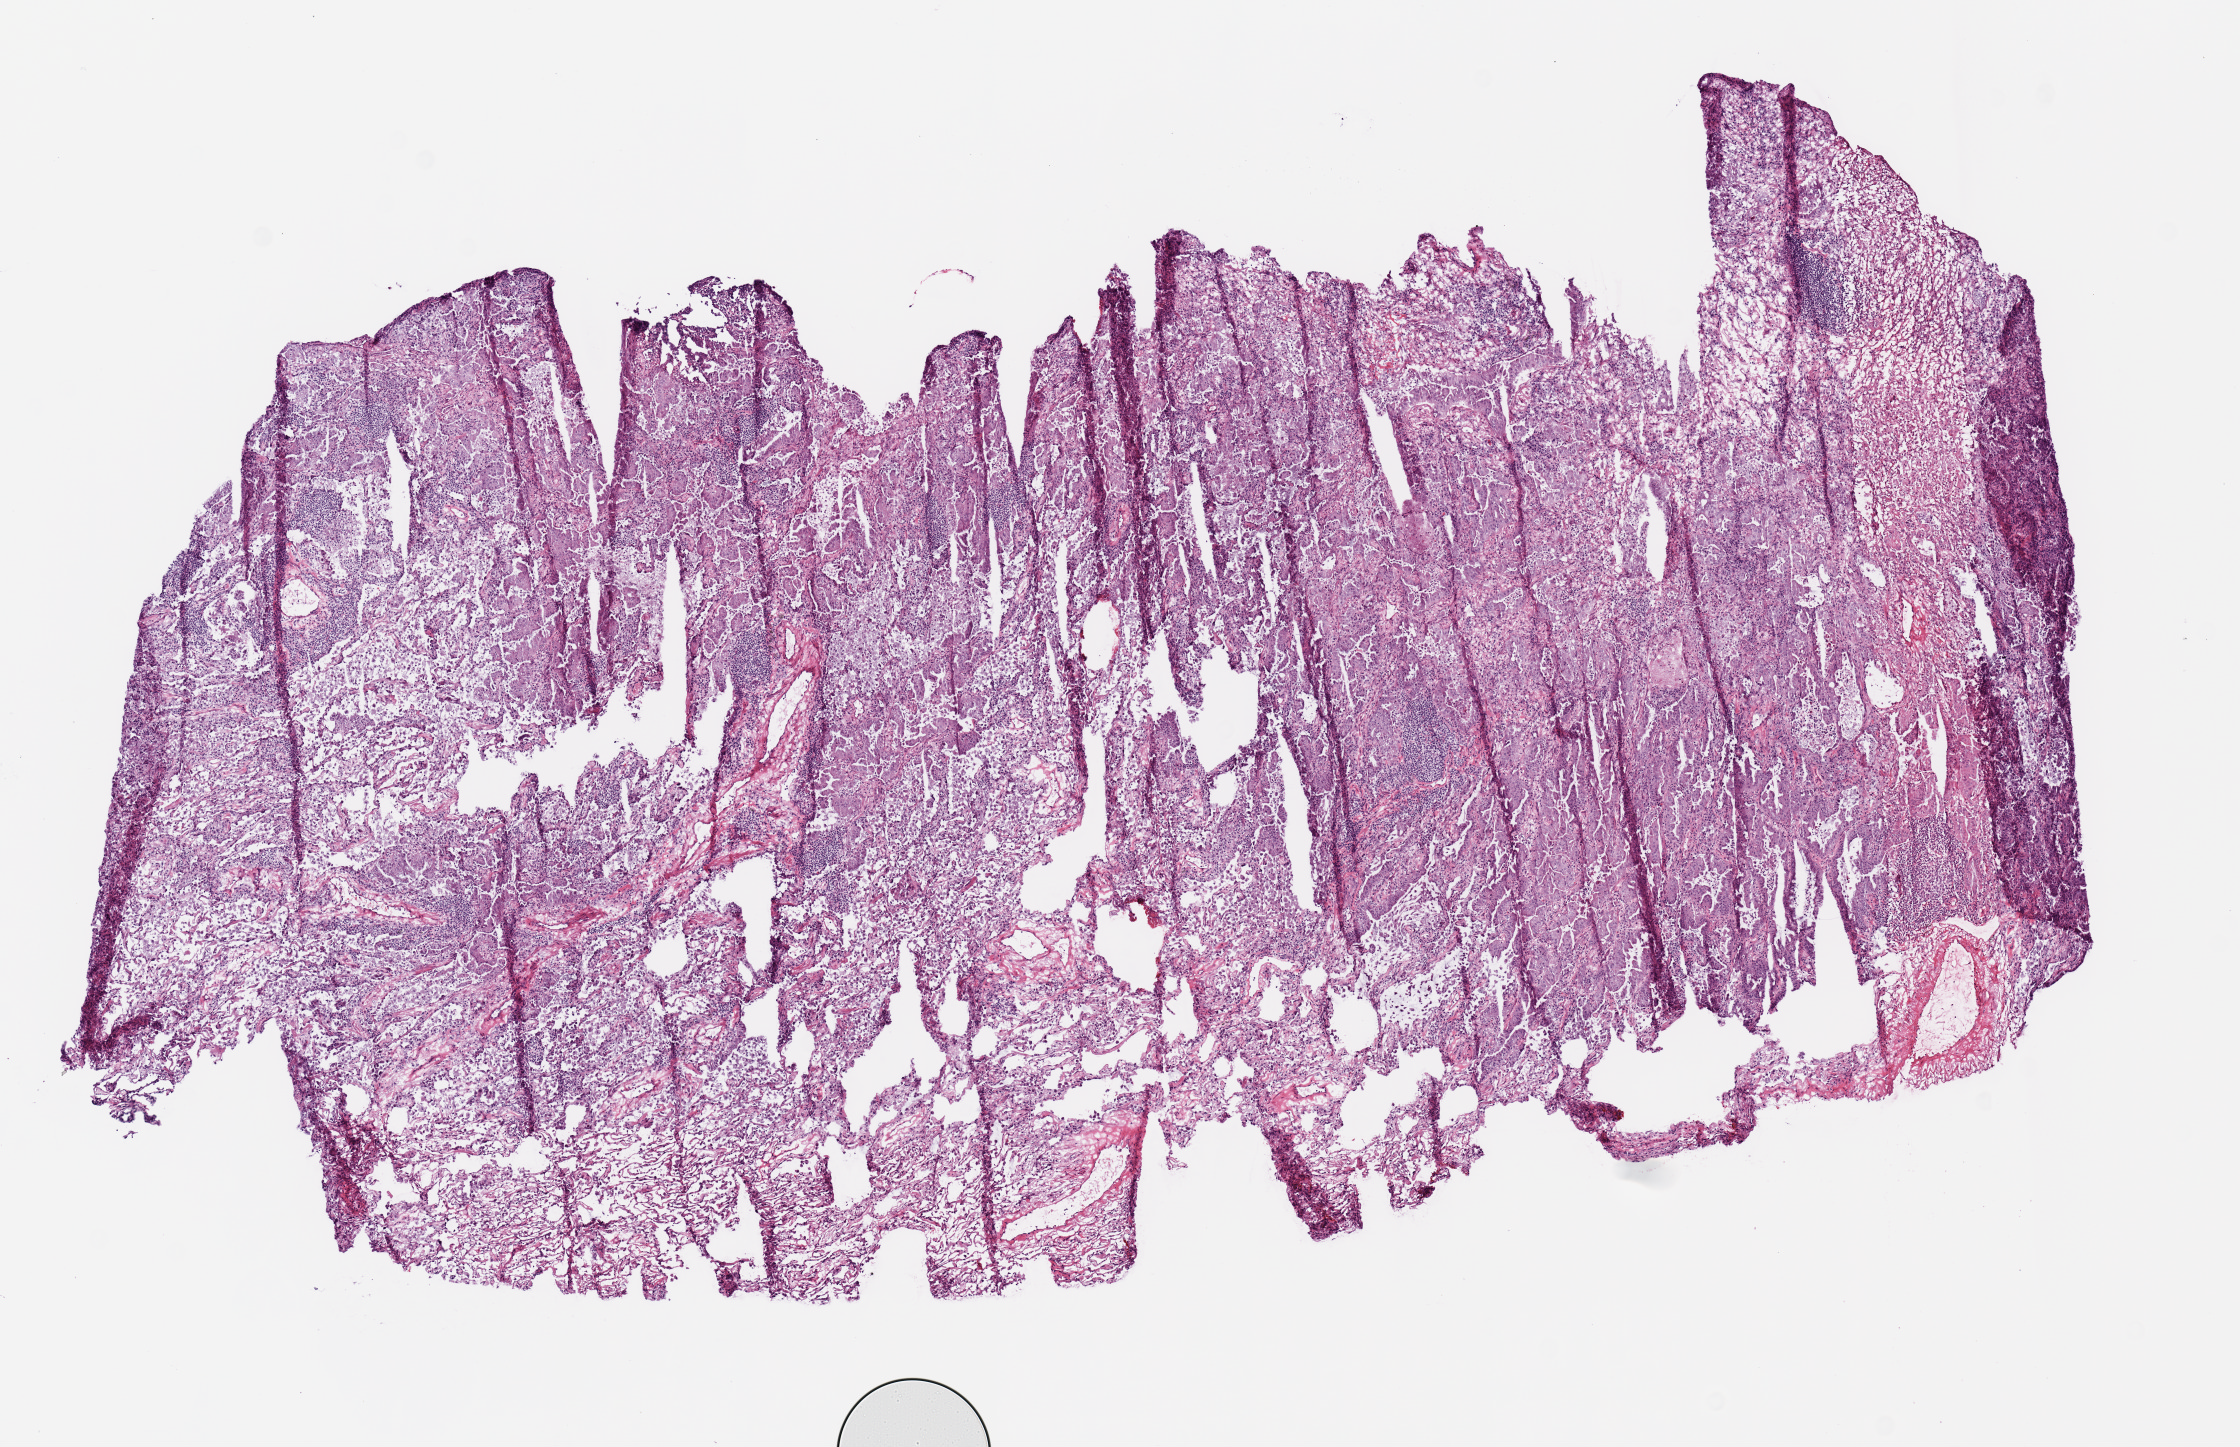
Digitized Hematoxylin and eosin (H&E) stained tissue section (whole slide) — whole scanned area (about 8.9 x 5.7 mm, from a 20x scan) shown as a low-resolution overview; frozen section from the top of the tissue portion; lung, primary tumour sample. Female patient; age at initial diagnosis 72 years. Slide review estimates, as recorded: tumour cells 72%, tumour nuclei 60%, normal cells 8%, stromal cells 15%, necrosis 5%.
• AJCC pathologic stage: IIB
• diagnosis: Mucinous adenocarcinoma (lower lobe, lung)
• laterality: right